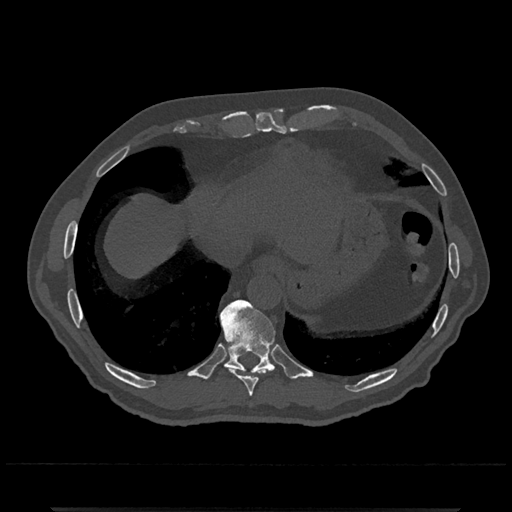
CT including the spine, one axial slice; slice 582 of 797 in the series (ordered by position); reconstruction kernel Br40s/3; bone window (W 1800 / L 400 HU); 0.5 mm slice thickness; 512 × 512 image matrix, field of view 393 × 393 mm. Patient: male, 67 years. Case-level facts recorded for this patient, not image findings: primary cancer: prostate.
Annotated regions visible in this slice (semi-automatically segmented with operator editing):
- T10 vertebra: bounding box <220,300,276,374> (left, top, right, bottom; pixels)
- T9 vertebra: <228,367,265,397>